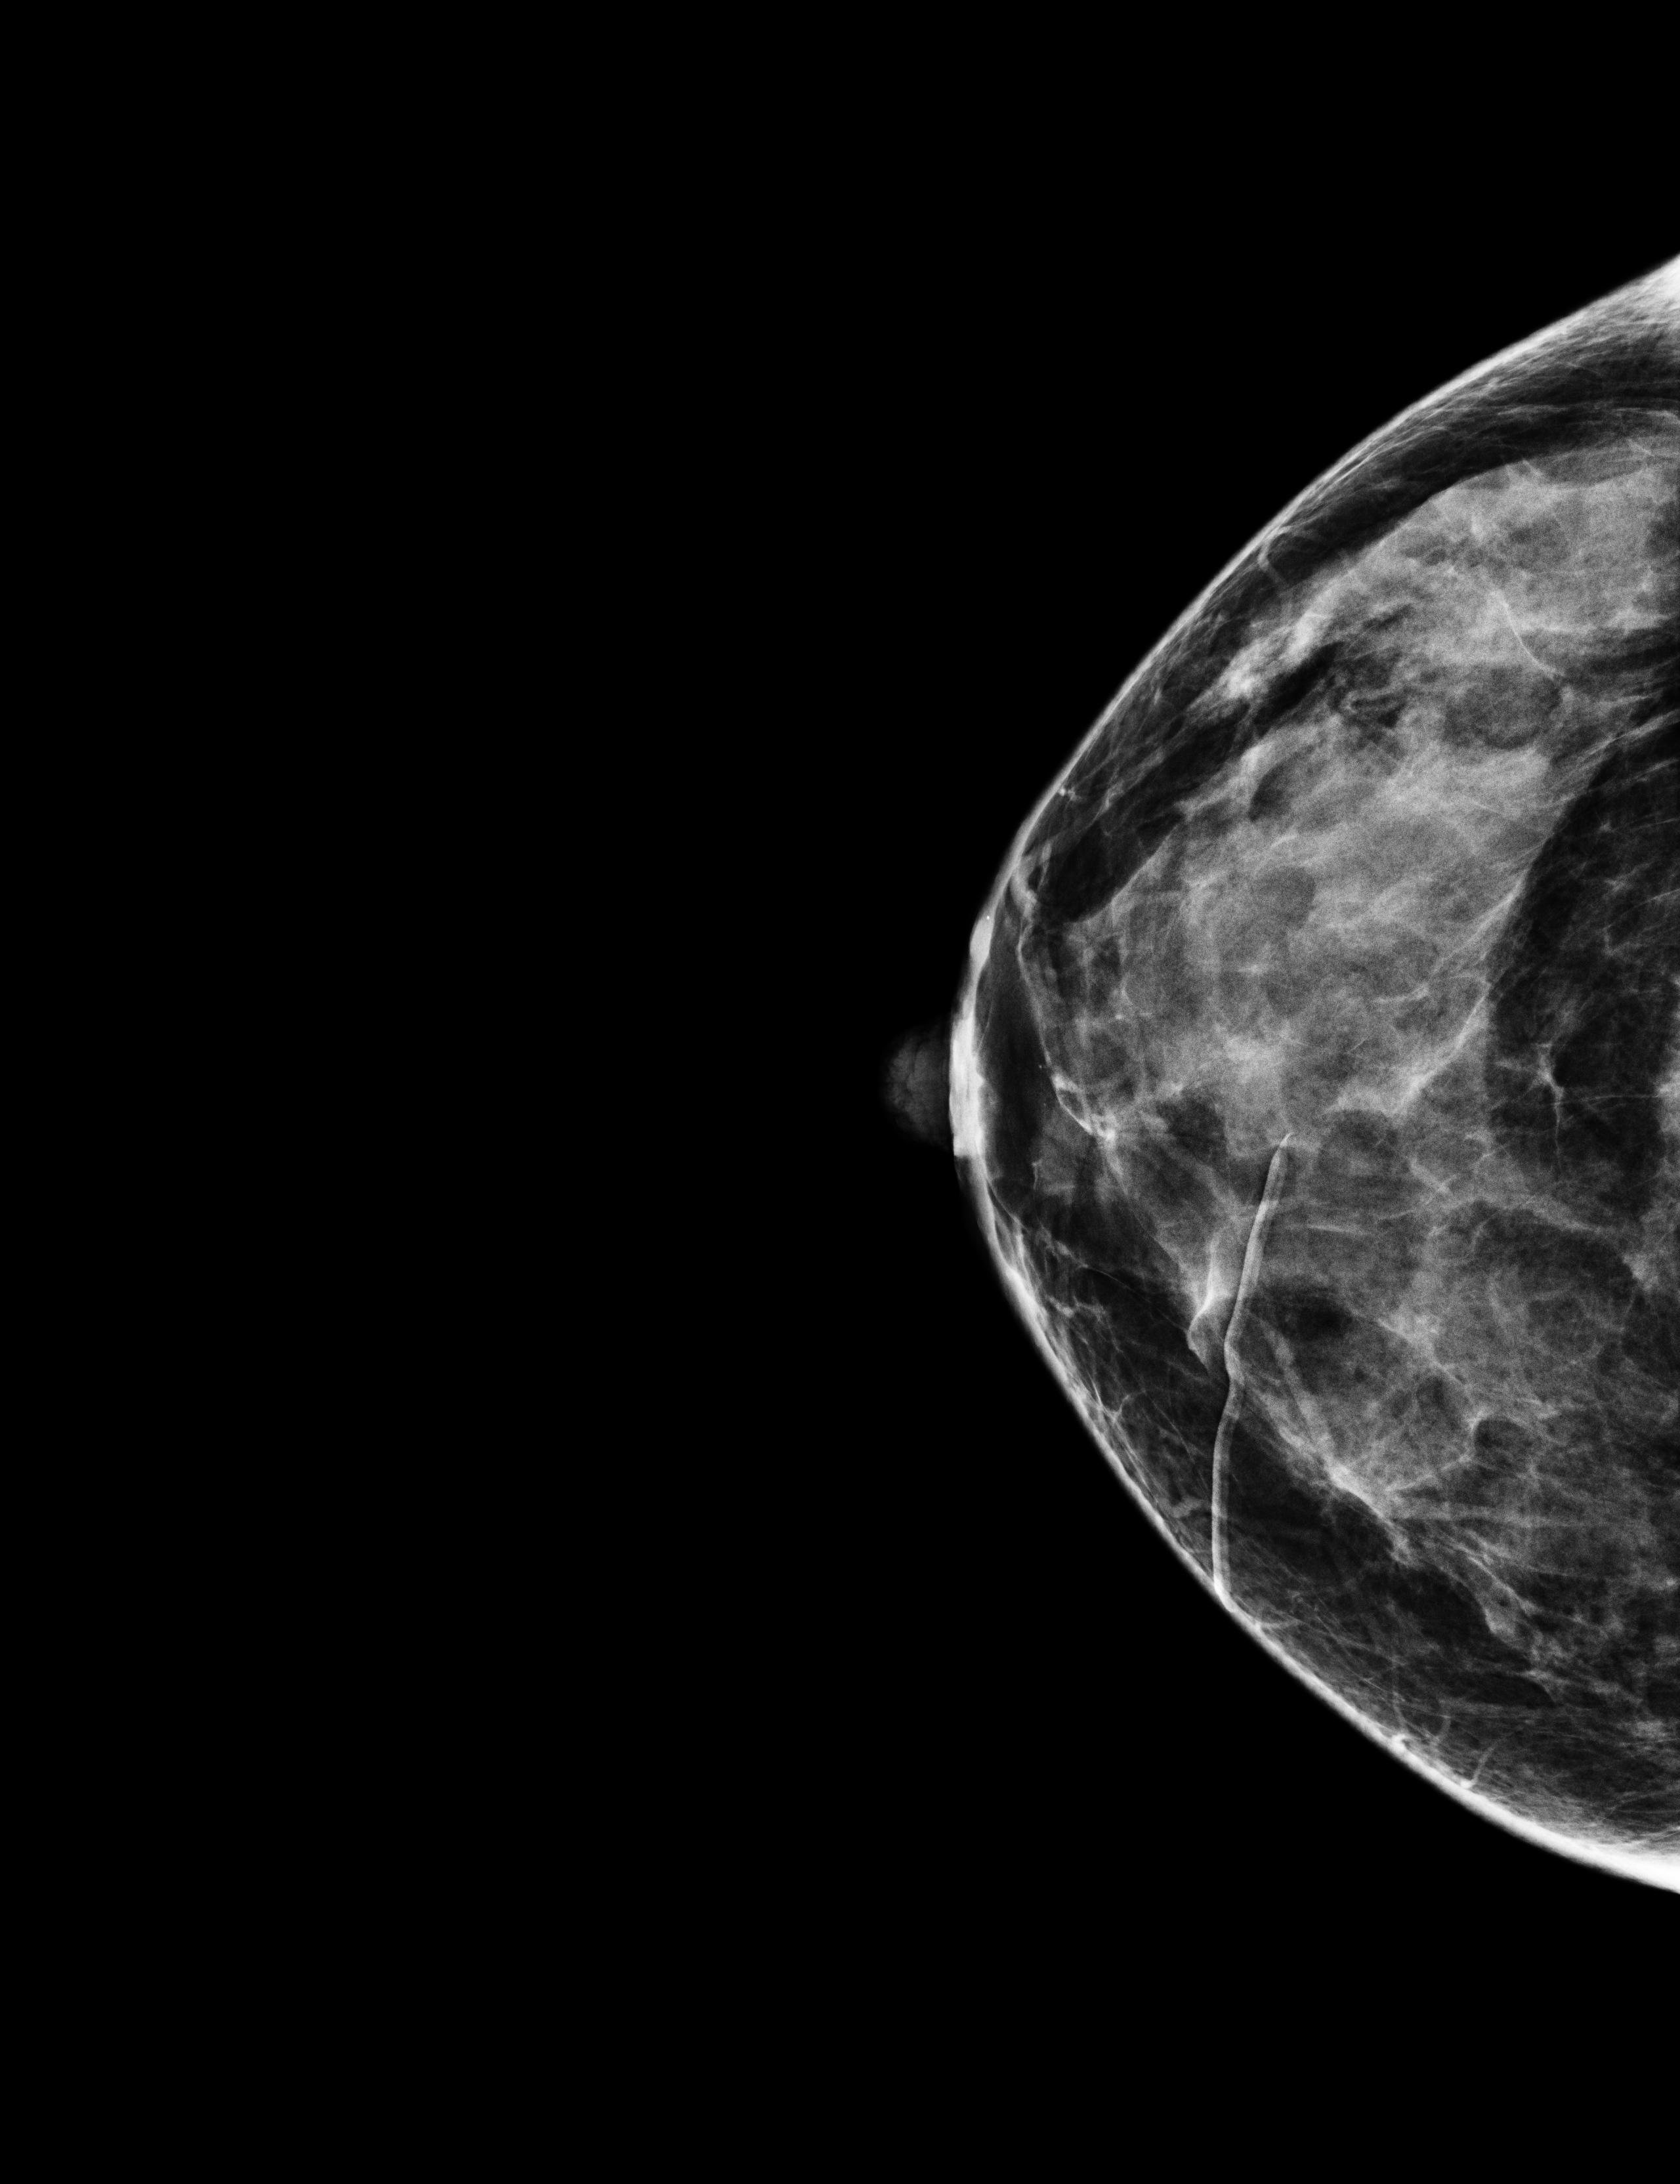
Digital mammogram (FFDM), right breast, CC view, screening examination. Female patient, age 49 years.
BI-RADS breast density category at the screening exam (both breasts, scale 1–4): 3. Final BI-RADS category for the screening round (tomosynthesis exam, both breasts): category 1. Recall: no recall after this screen.